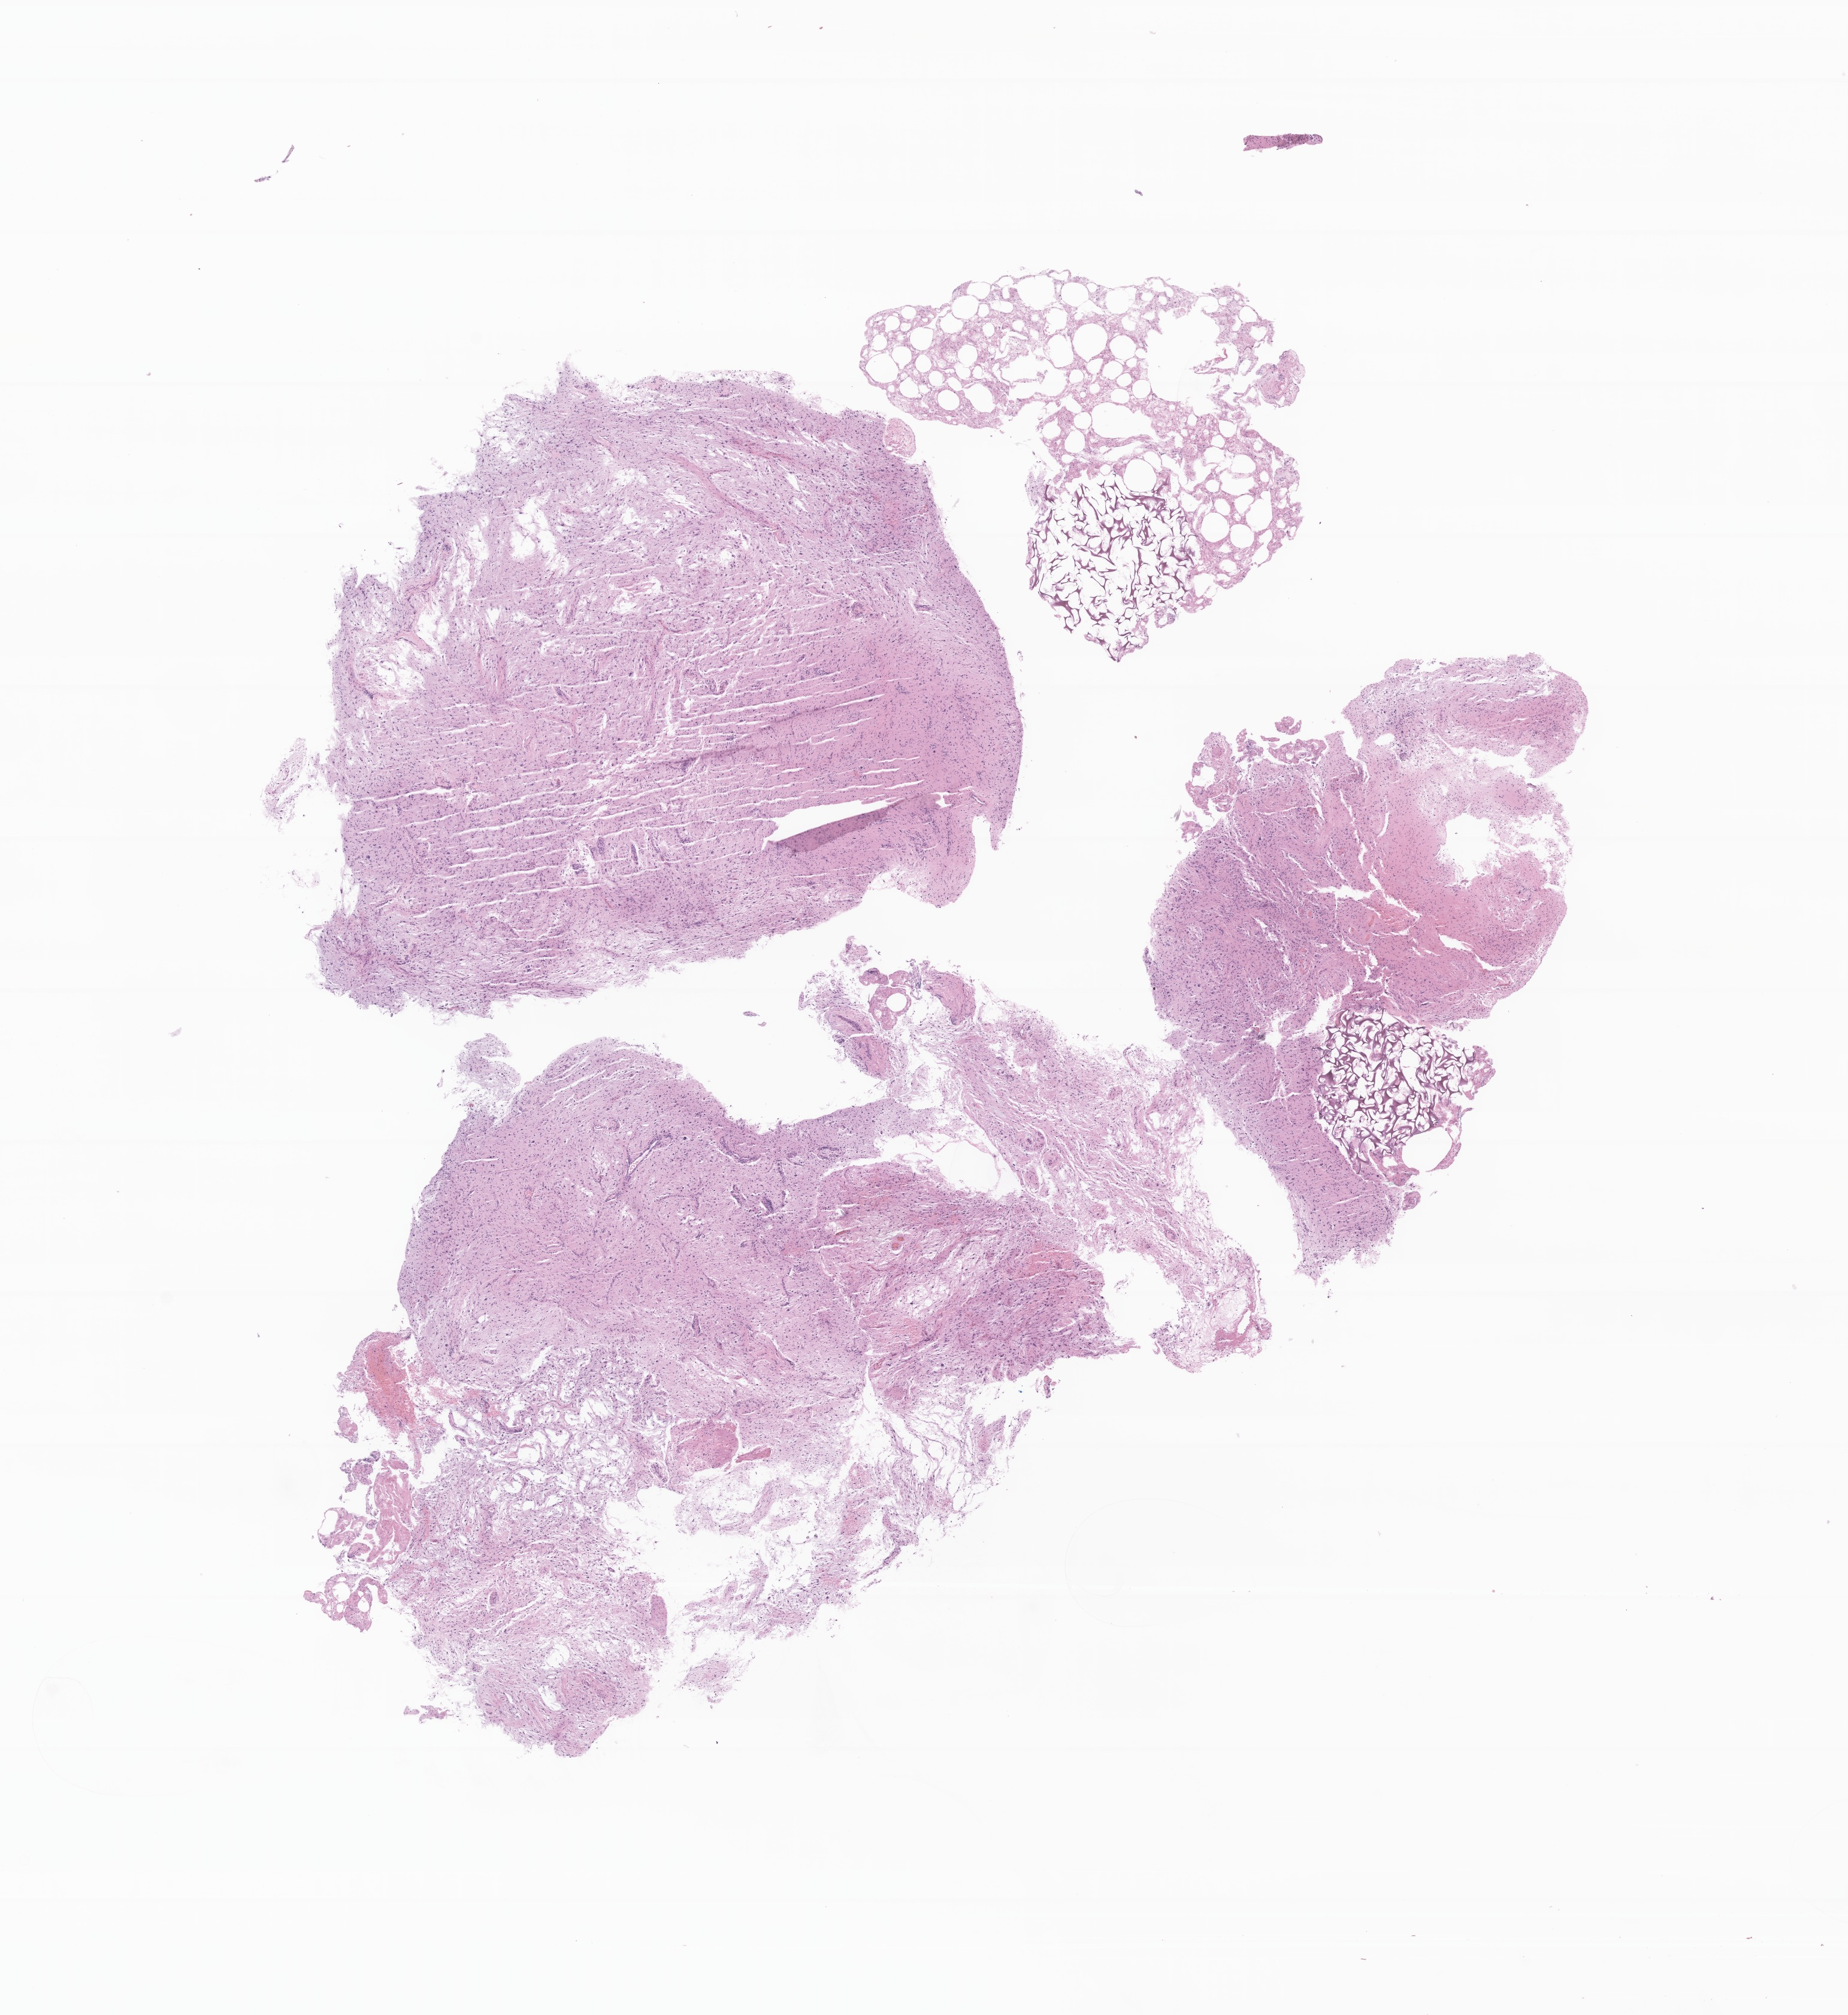
Whole-slide image, hematoxylin and eosin (H&E) stain of tumor tissue from the brain, whole scanned area (about 13.0 x 14.2 mm) shown as a low-resolution overview. Formalin-fixed paraffin-embedded section. Patient: female, age 170 months (14 years 2 months).
Diagnosis: Neoplasm, uncertain whether benign or malignant.